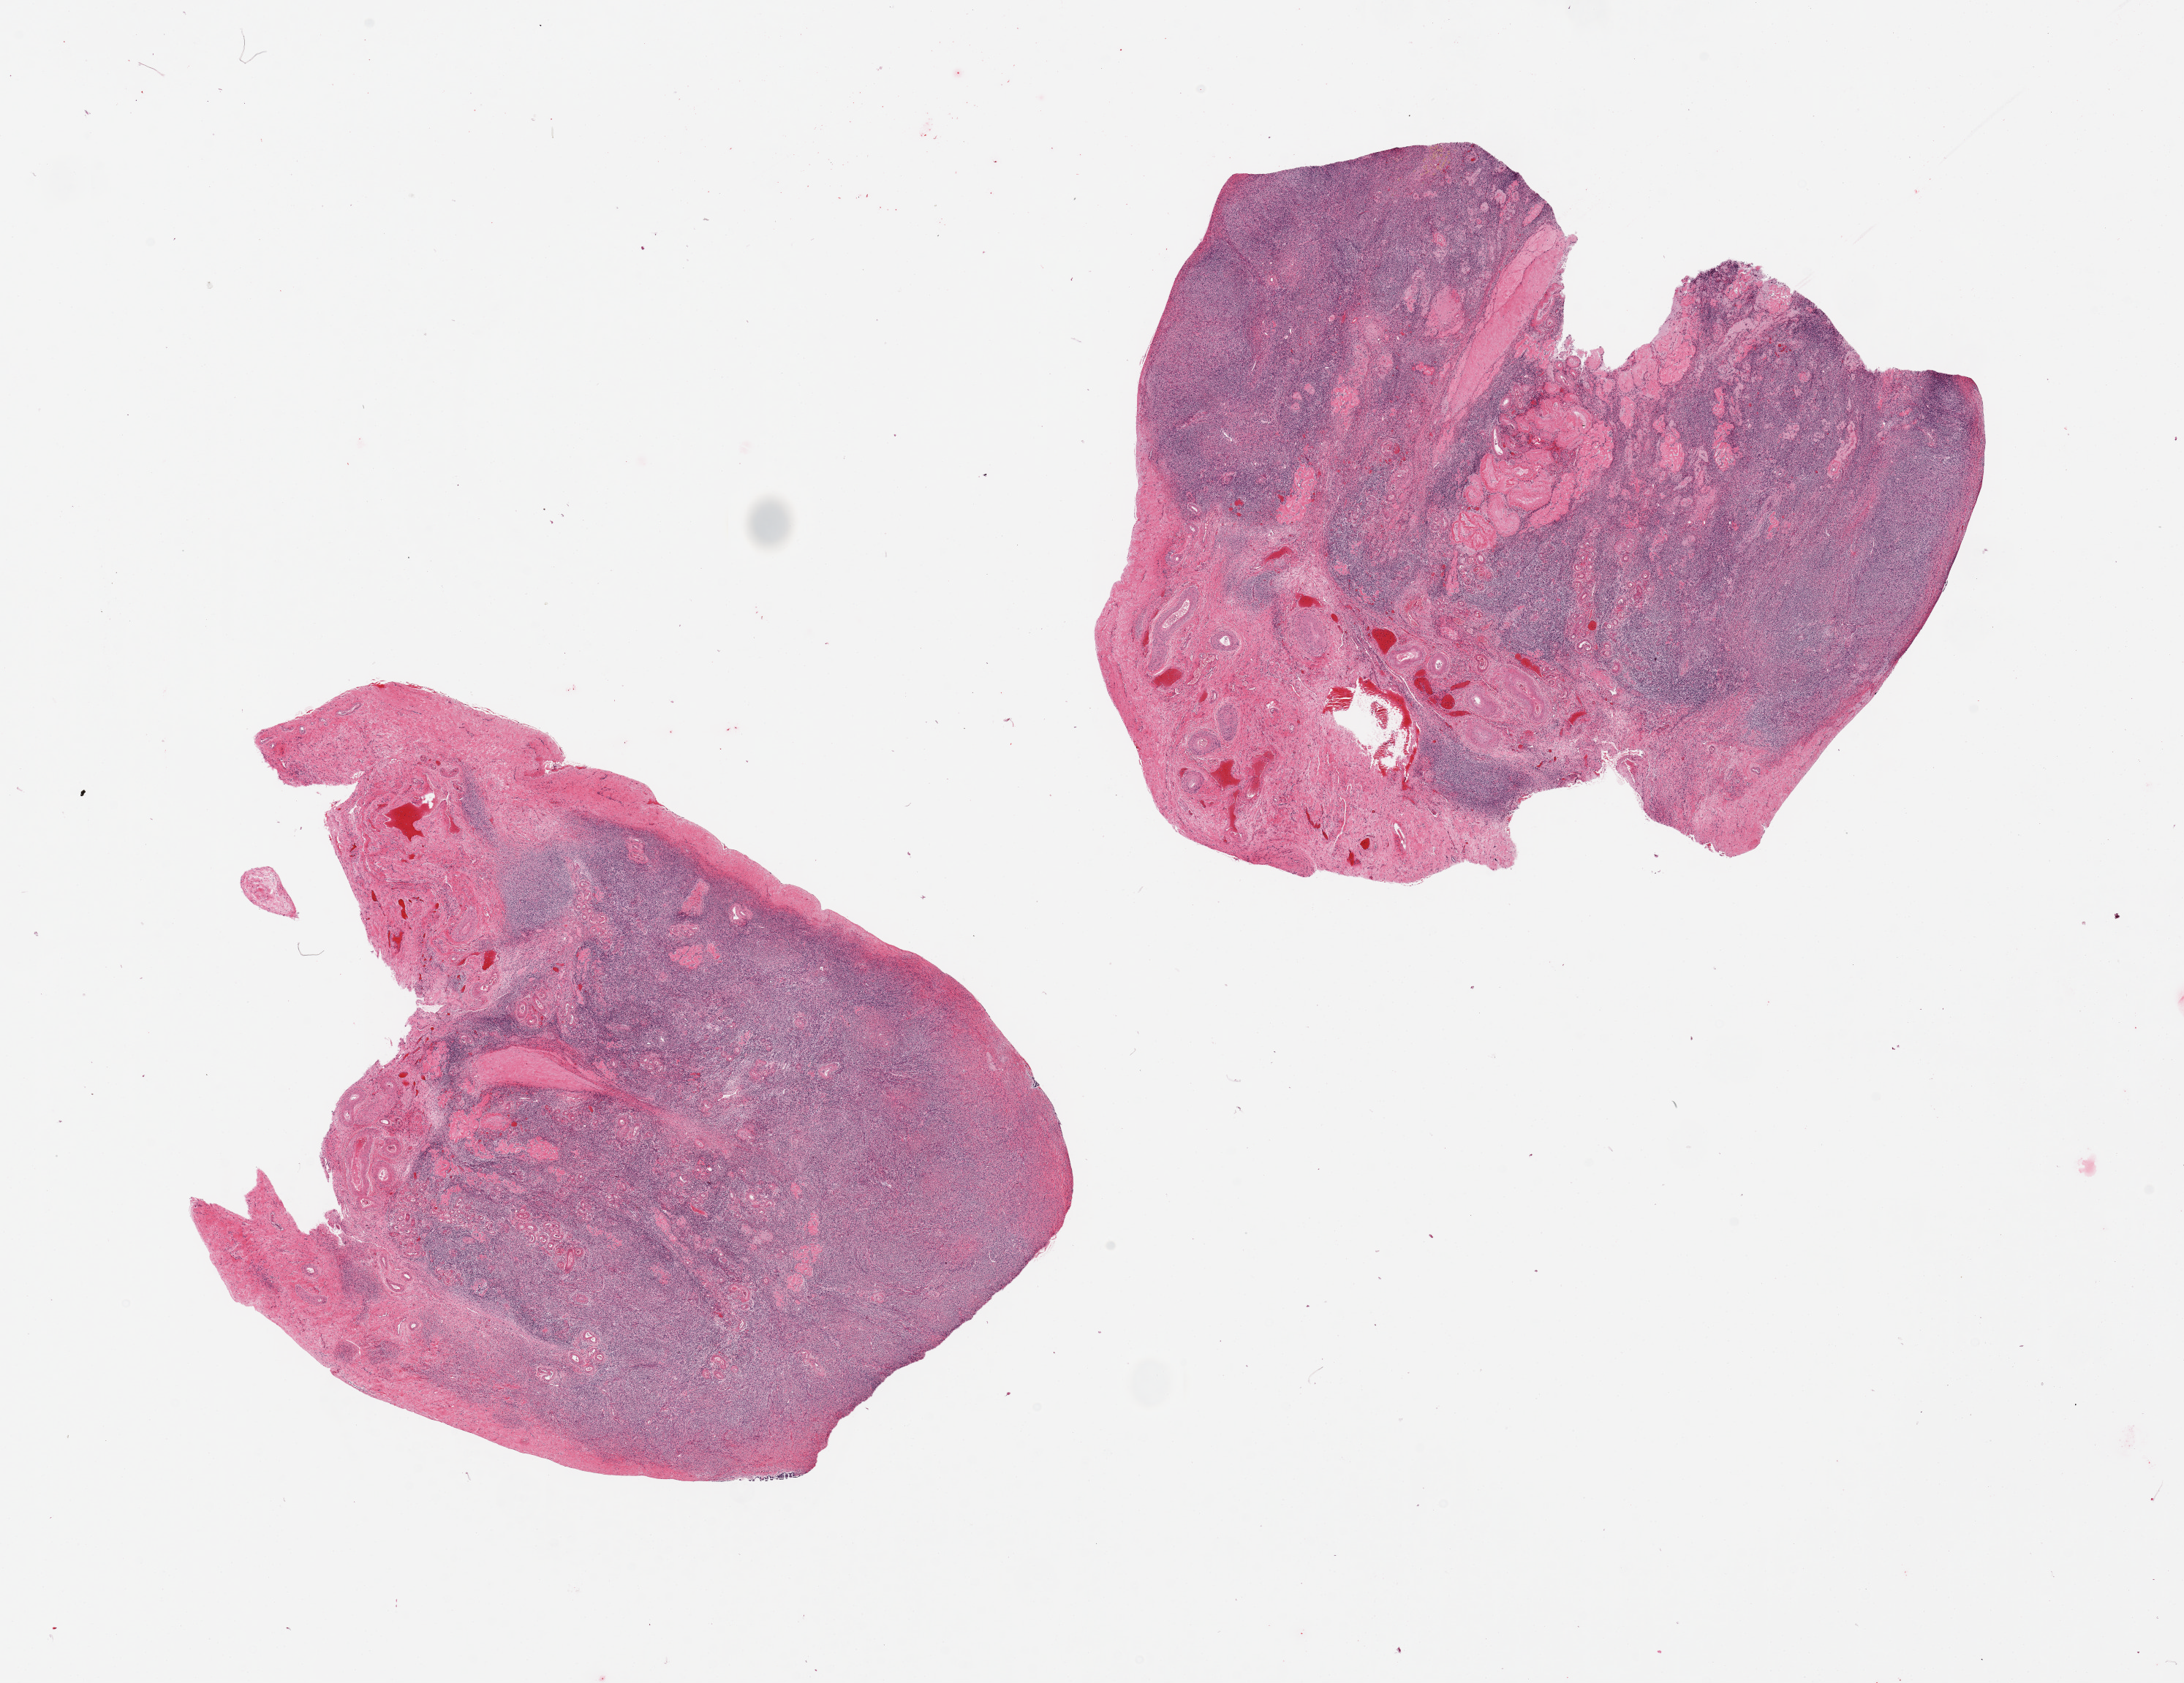
H&E whole-slide image — shown as a low-resolution overview of the whole scanned area (about 23.6 x 18.2 mm, slide scanned at 20x). PAXgene-fixed, paraffin-embedded tissue. Sampled site (target tissue): ovary. Donor tissue sample. Donor: female.
Pathologist's review note for this sample: 2 pieces, post menopausal involution/atrophy.